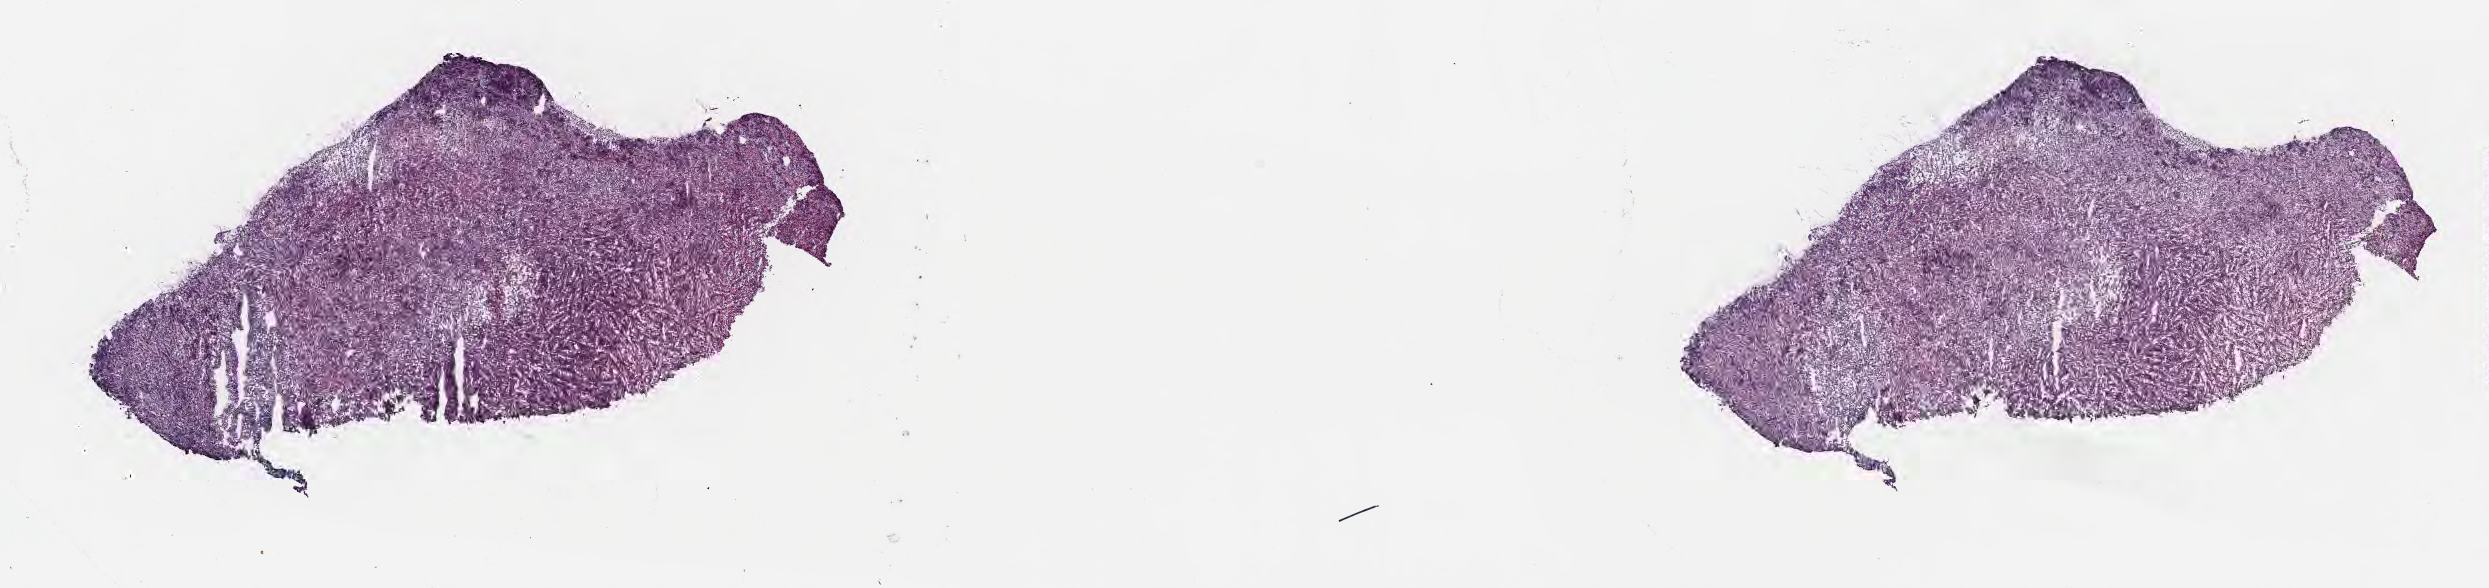
Whole-slide image, haematoxylin and eosin stain, a low-resolution overview of the entire scanned area, about 20.1 x 4.8 mm; cryosection; primary tumor; site: mandible. Patient: male, age at initial diagnosis 8 years. Pathologist review of this section (percent, as recorded): tumor cells 90%, tumor nuclei 95%, stromal cells 5%, necrosis 0%, normal cells 5%. Infiltration values recorded for this section: lymphocyte infiltration 50%, monocyte infiltration 25%, neutrophil infiltration 5%.
• diagnosis: Burkitt lymphoma, NOS
• section: top of the tissue portion
• Ann Arbor stage (patient): Stage II